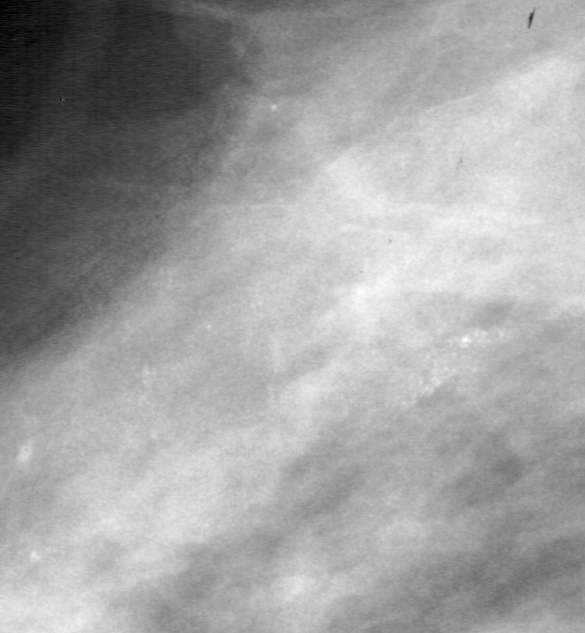
Cropped region of a digitized screen-film mammogram centred on a radiologist-marked abnormality, left breast, MLO view.
Marked abnormality: calcifications, morphology pleomorphic, distribution clustered; BI-RADS assessment category 4; subtlety rating 2 on a 1 (subtle) to 5 (obvious) scale; pathology (as recorded): benign.